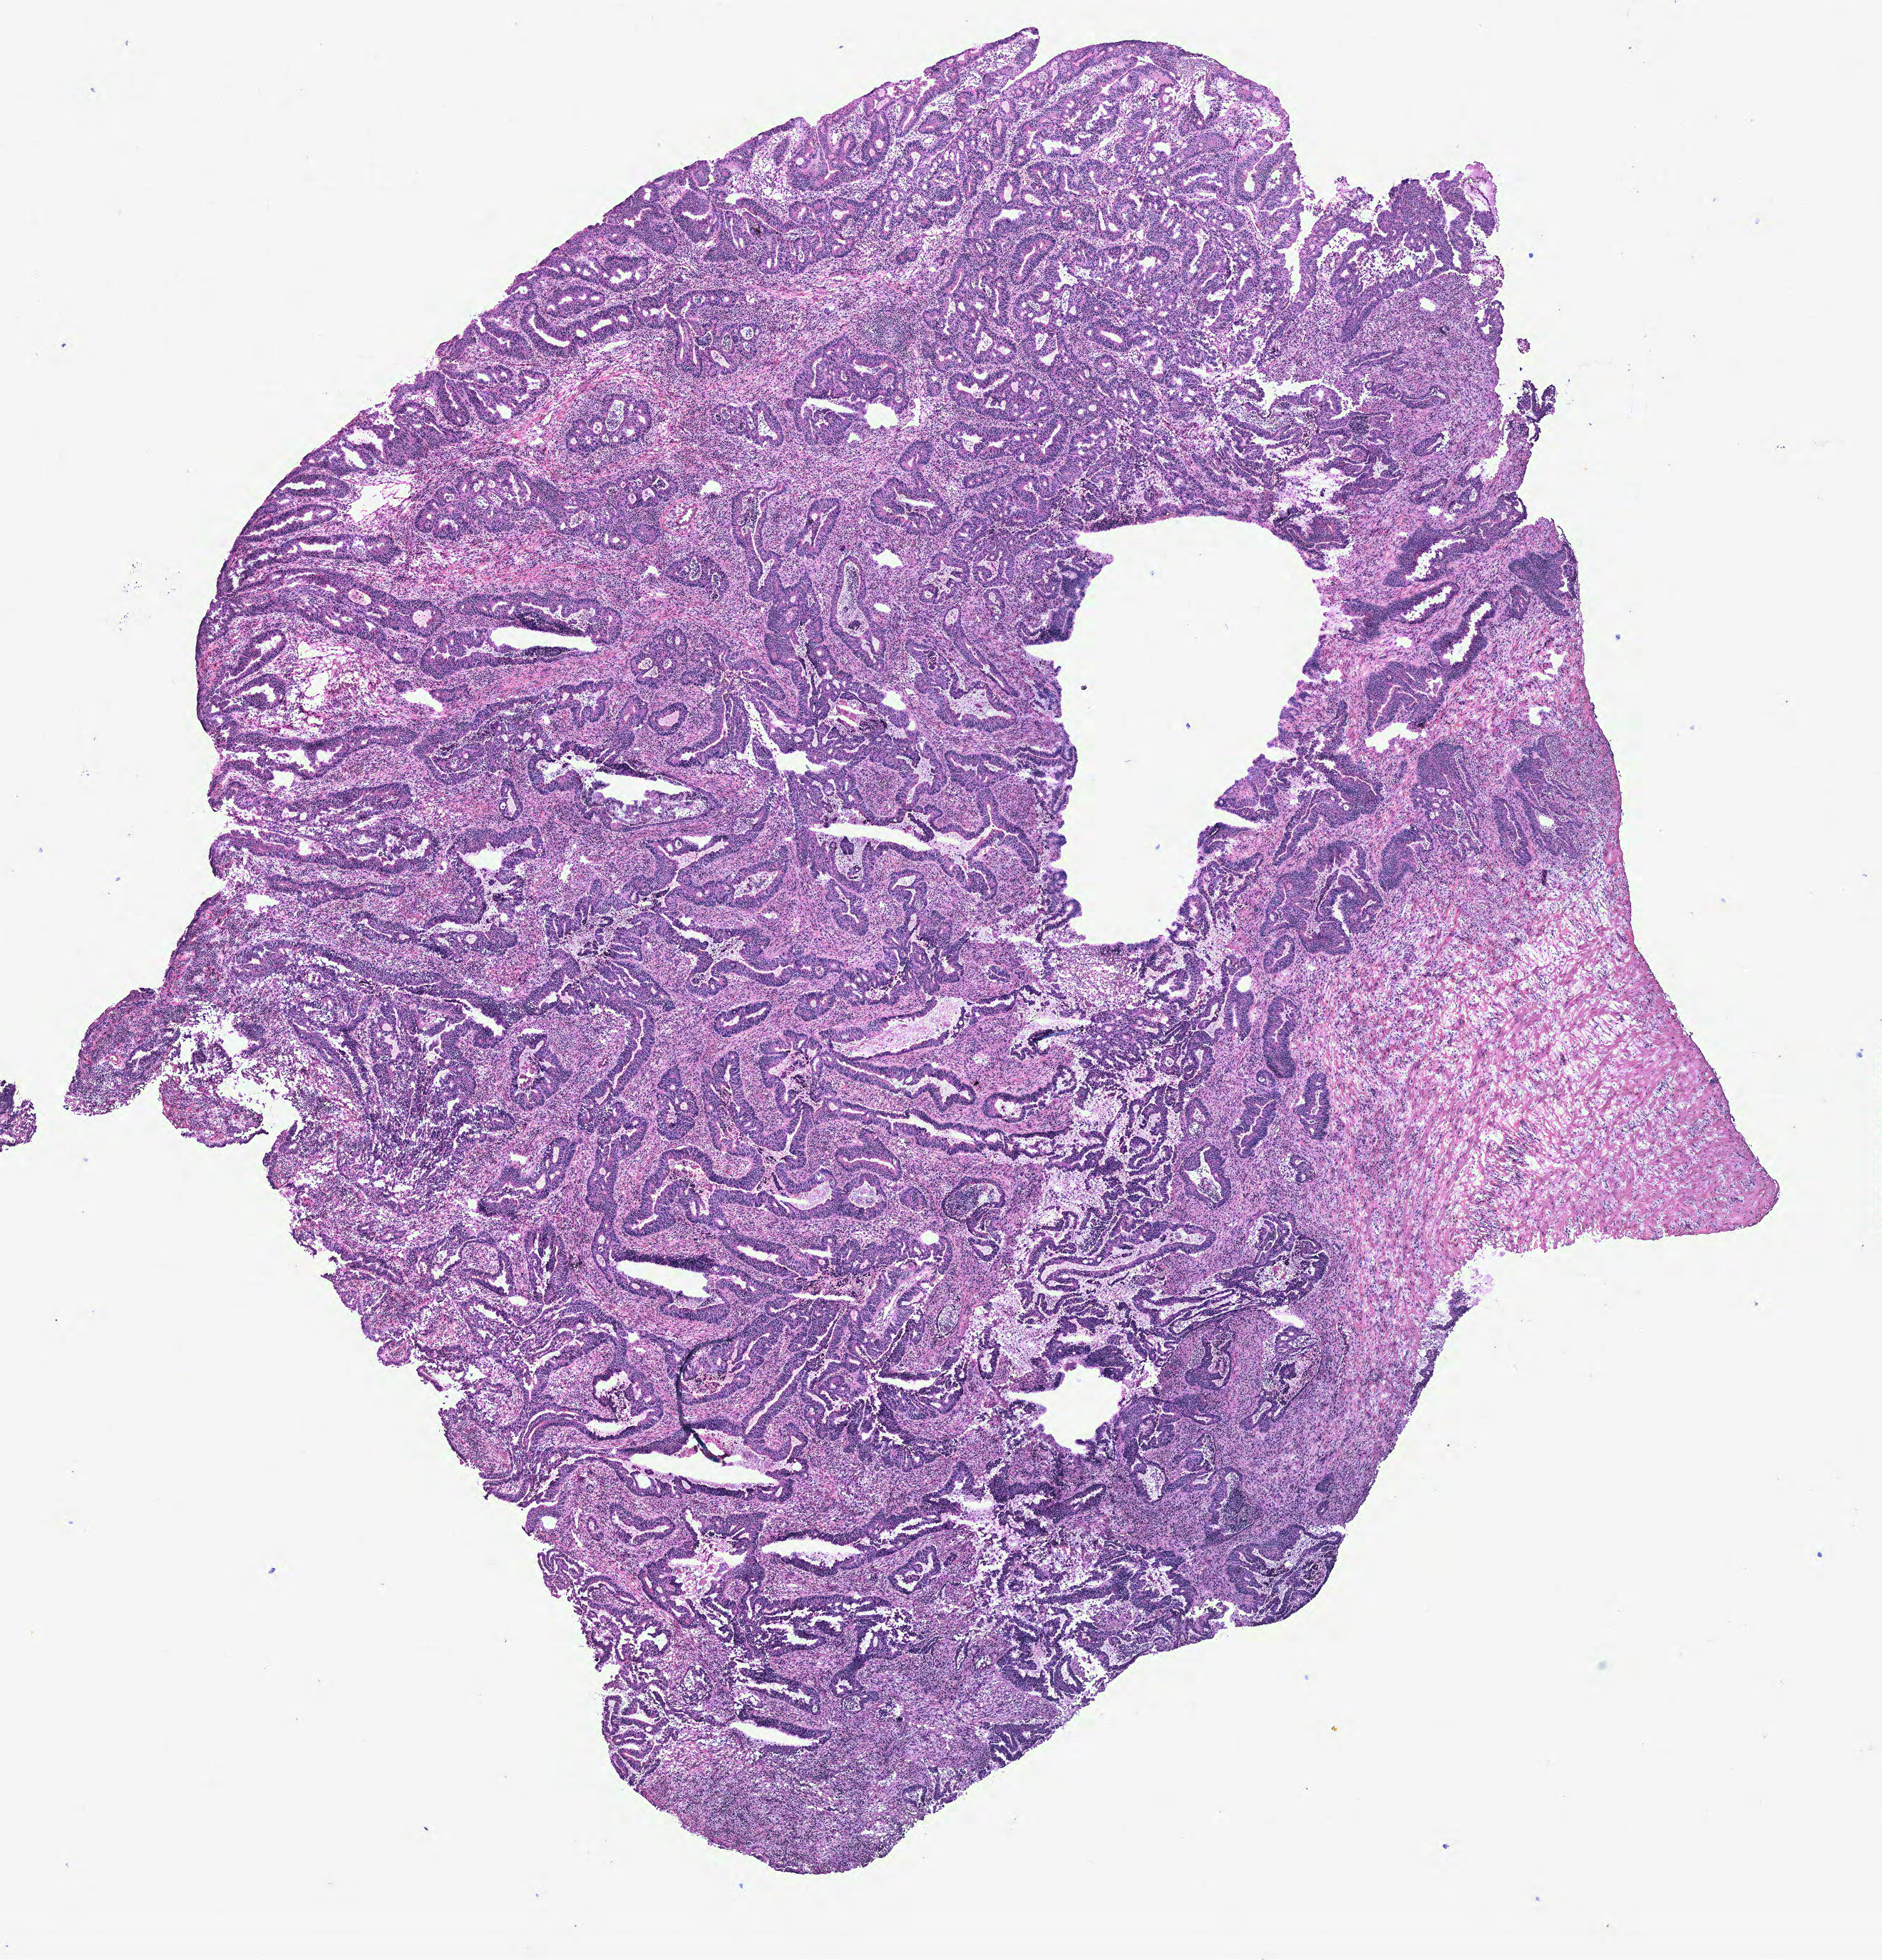
H&E whole-slide image, low-resolution overview of the scanned area, about 10.6 x 11.0 mm; colon, tissue type not recorded.
• patient diagnosis (cohort enrolment): colon cancer (colon)